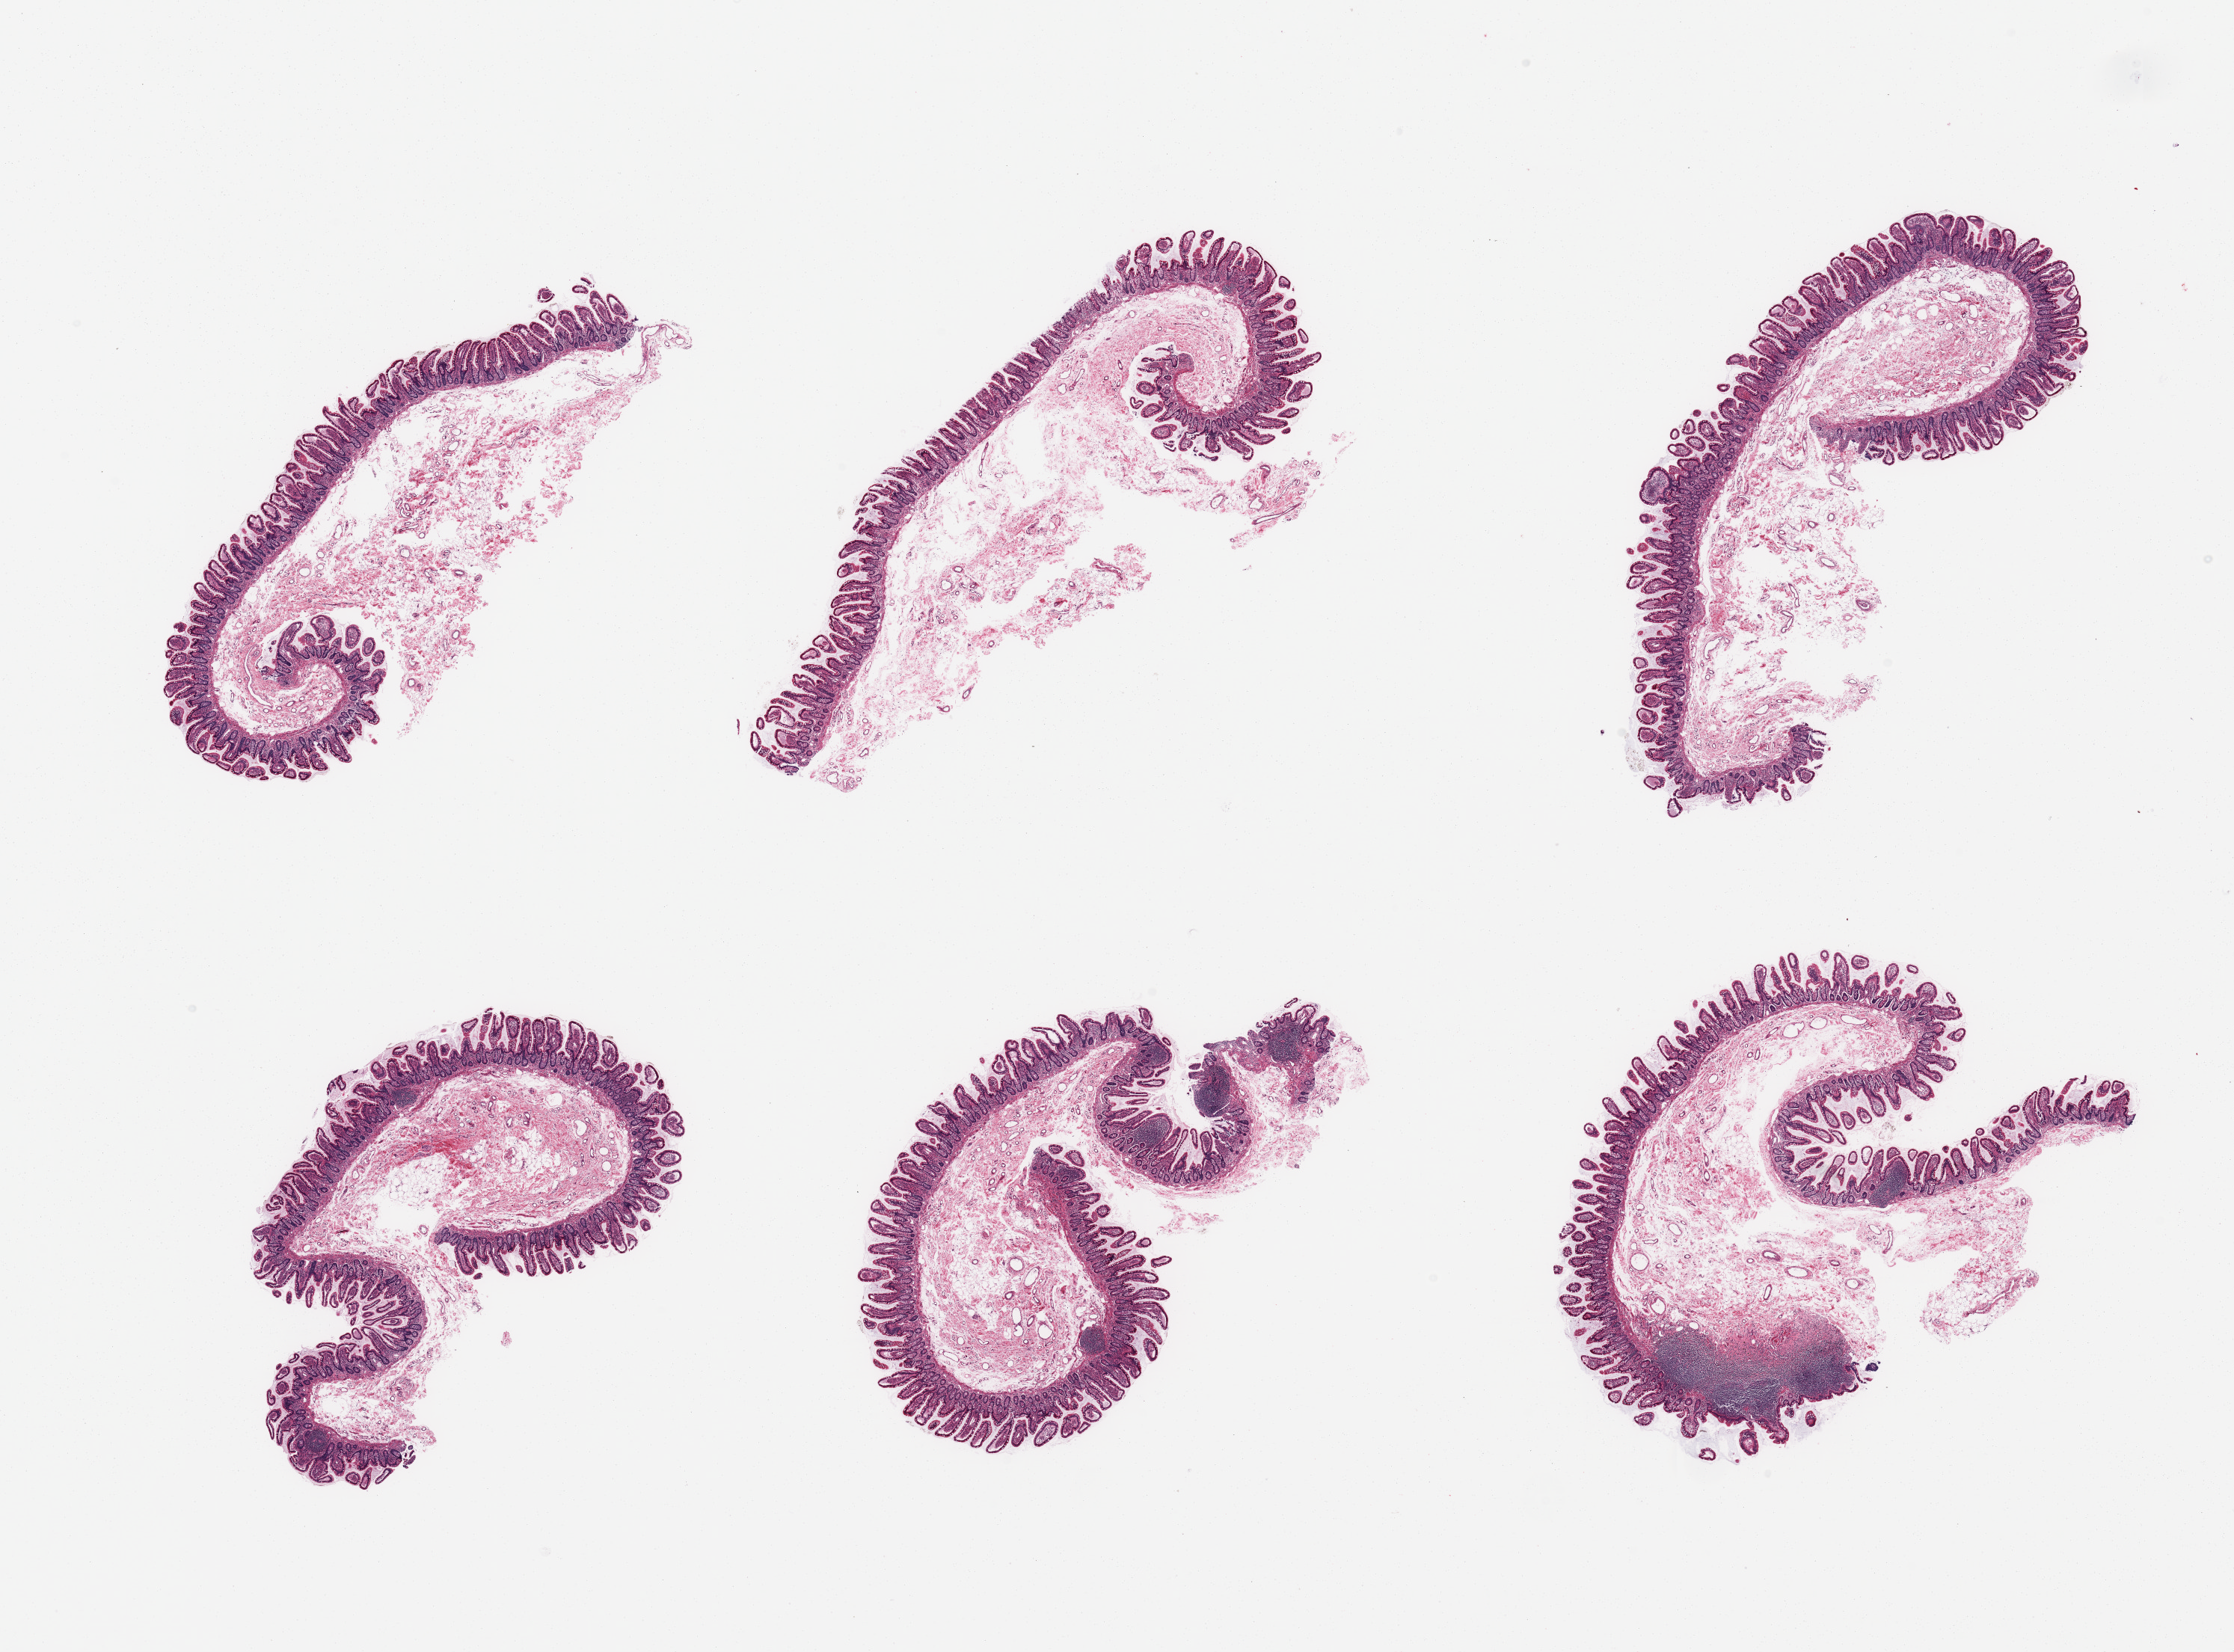
Whole-slide image, hematoxylin and eosin (H&E) stain, a low-resolution overview of the entire scanned area, about 23.6 x 17.5 mm. Male donor.
Specimen: PAXgene-fixed, paraffin-embedded tissue; section of ileum (target tissue); tissue donor sample.